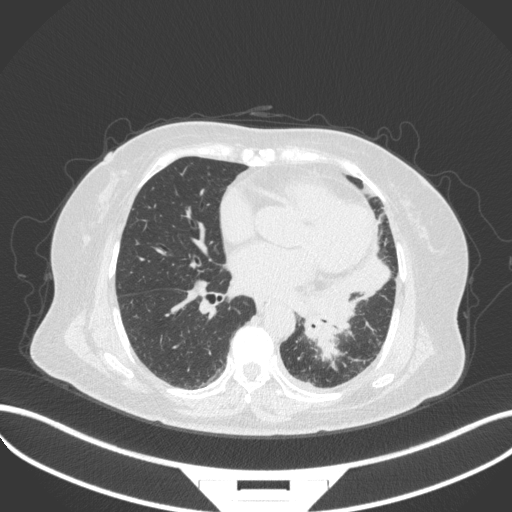
Chest CT, one axial slice; position 156 of 328 along the scan axis; 120 kVp; lung window (W 1500 / L -600 HU); 1 mm slice thickness; 512 × 512 image matrix. Patient: female, 69 years. From the clinical record (not read from this slice): clinical TNM (as recorded): T2b N3 M1.
Outlined on this slice (bounding box drawn by a radiologist):
- lung tumour (recorded histology: adenocarcinoma): box from (x=293, y=273) to (x=356, y=364) px